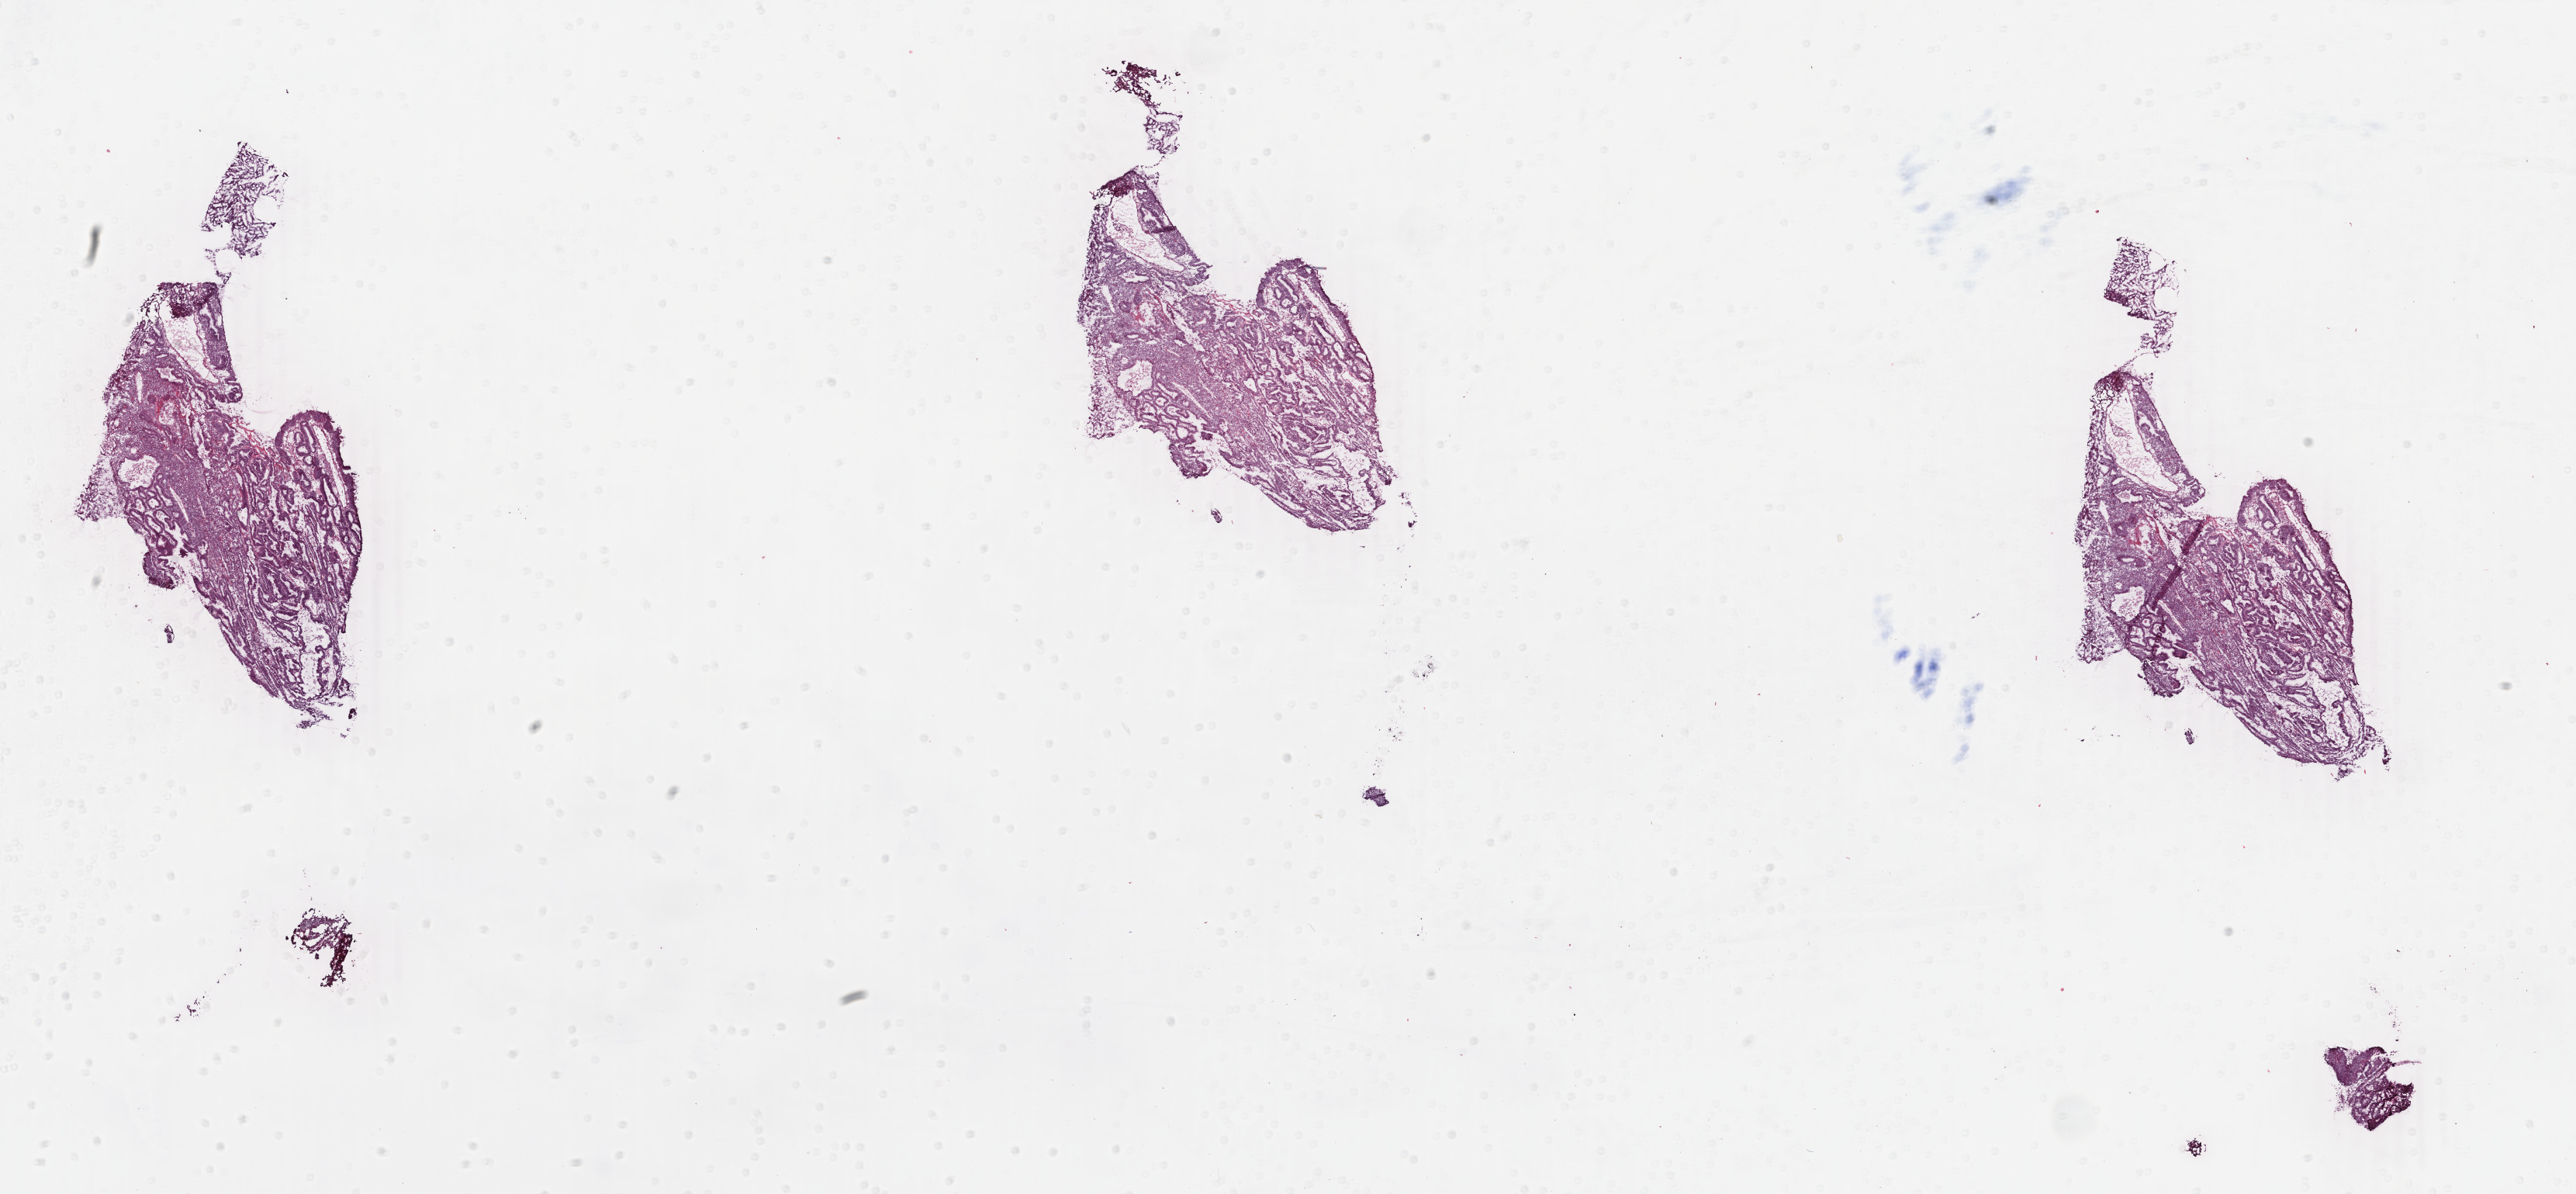
H&E whole-slide image, whole scanned area (about 26.4 x 12.2 mm, slide scanned at 40x) shown as a low-resolution overview. Frozen section. Sample: primary tumour, uterus. Female, age 57 years at initial diagnosis. Histologic grade: G1 (well differentiated). Slide review estimates, as recorded: tumour cells 92%, tumour nuclei 92%, normal cells 0%, stromal cells 5%, necrosis 3%. Infiltration values recorded for this section: lymphocyte infiltration 0%, monocyte infiltration 0%, neutrophil infiltration 5%.
Histologic diagnosis: Endometrioid adenocarcinoma, NOS (endometrium). FIGO stage: IB. Lymph nodes positive (case pathology): 0 of 24 examined.